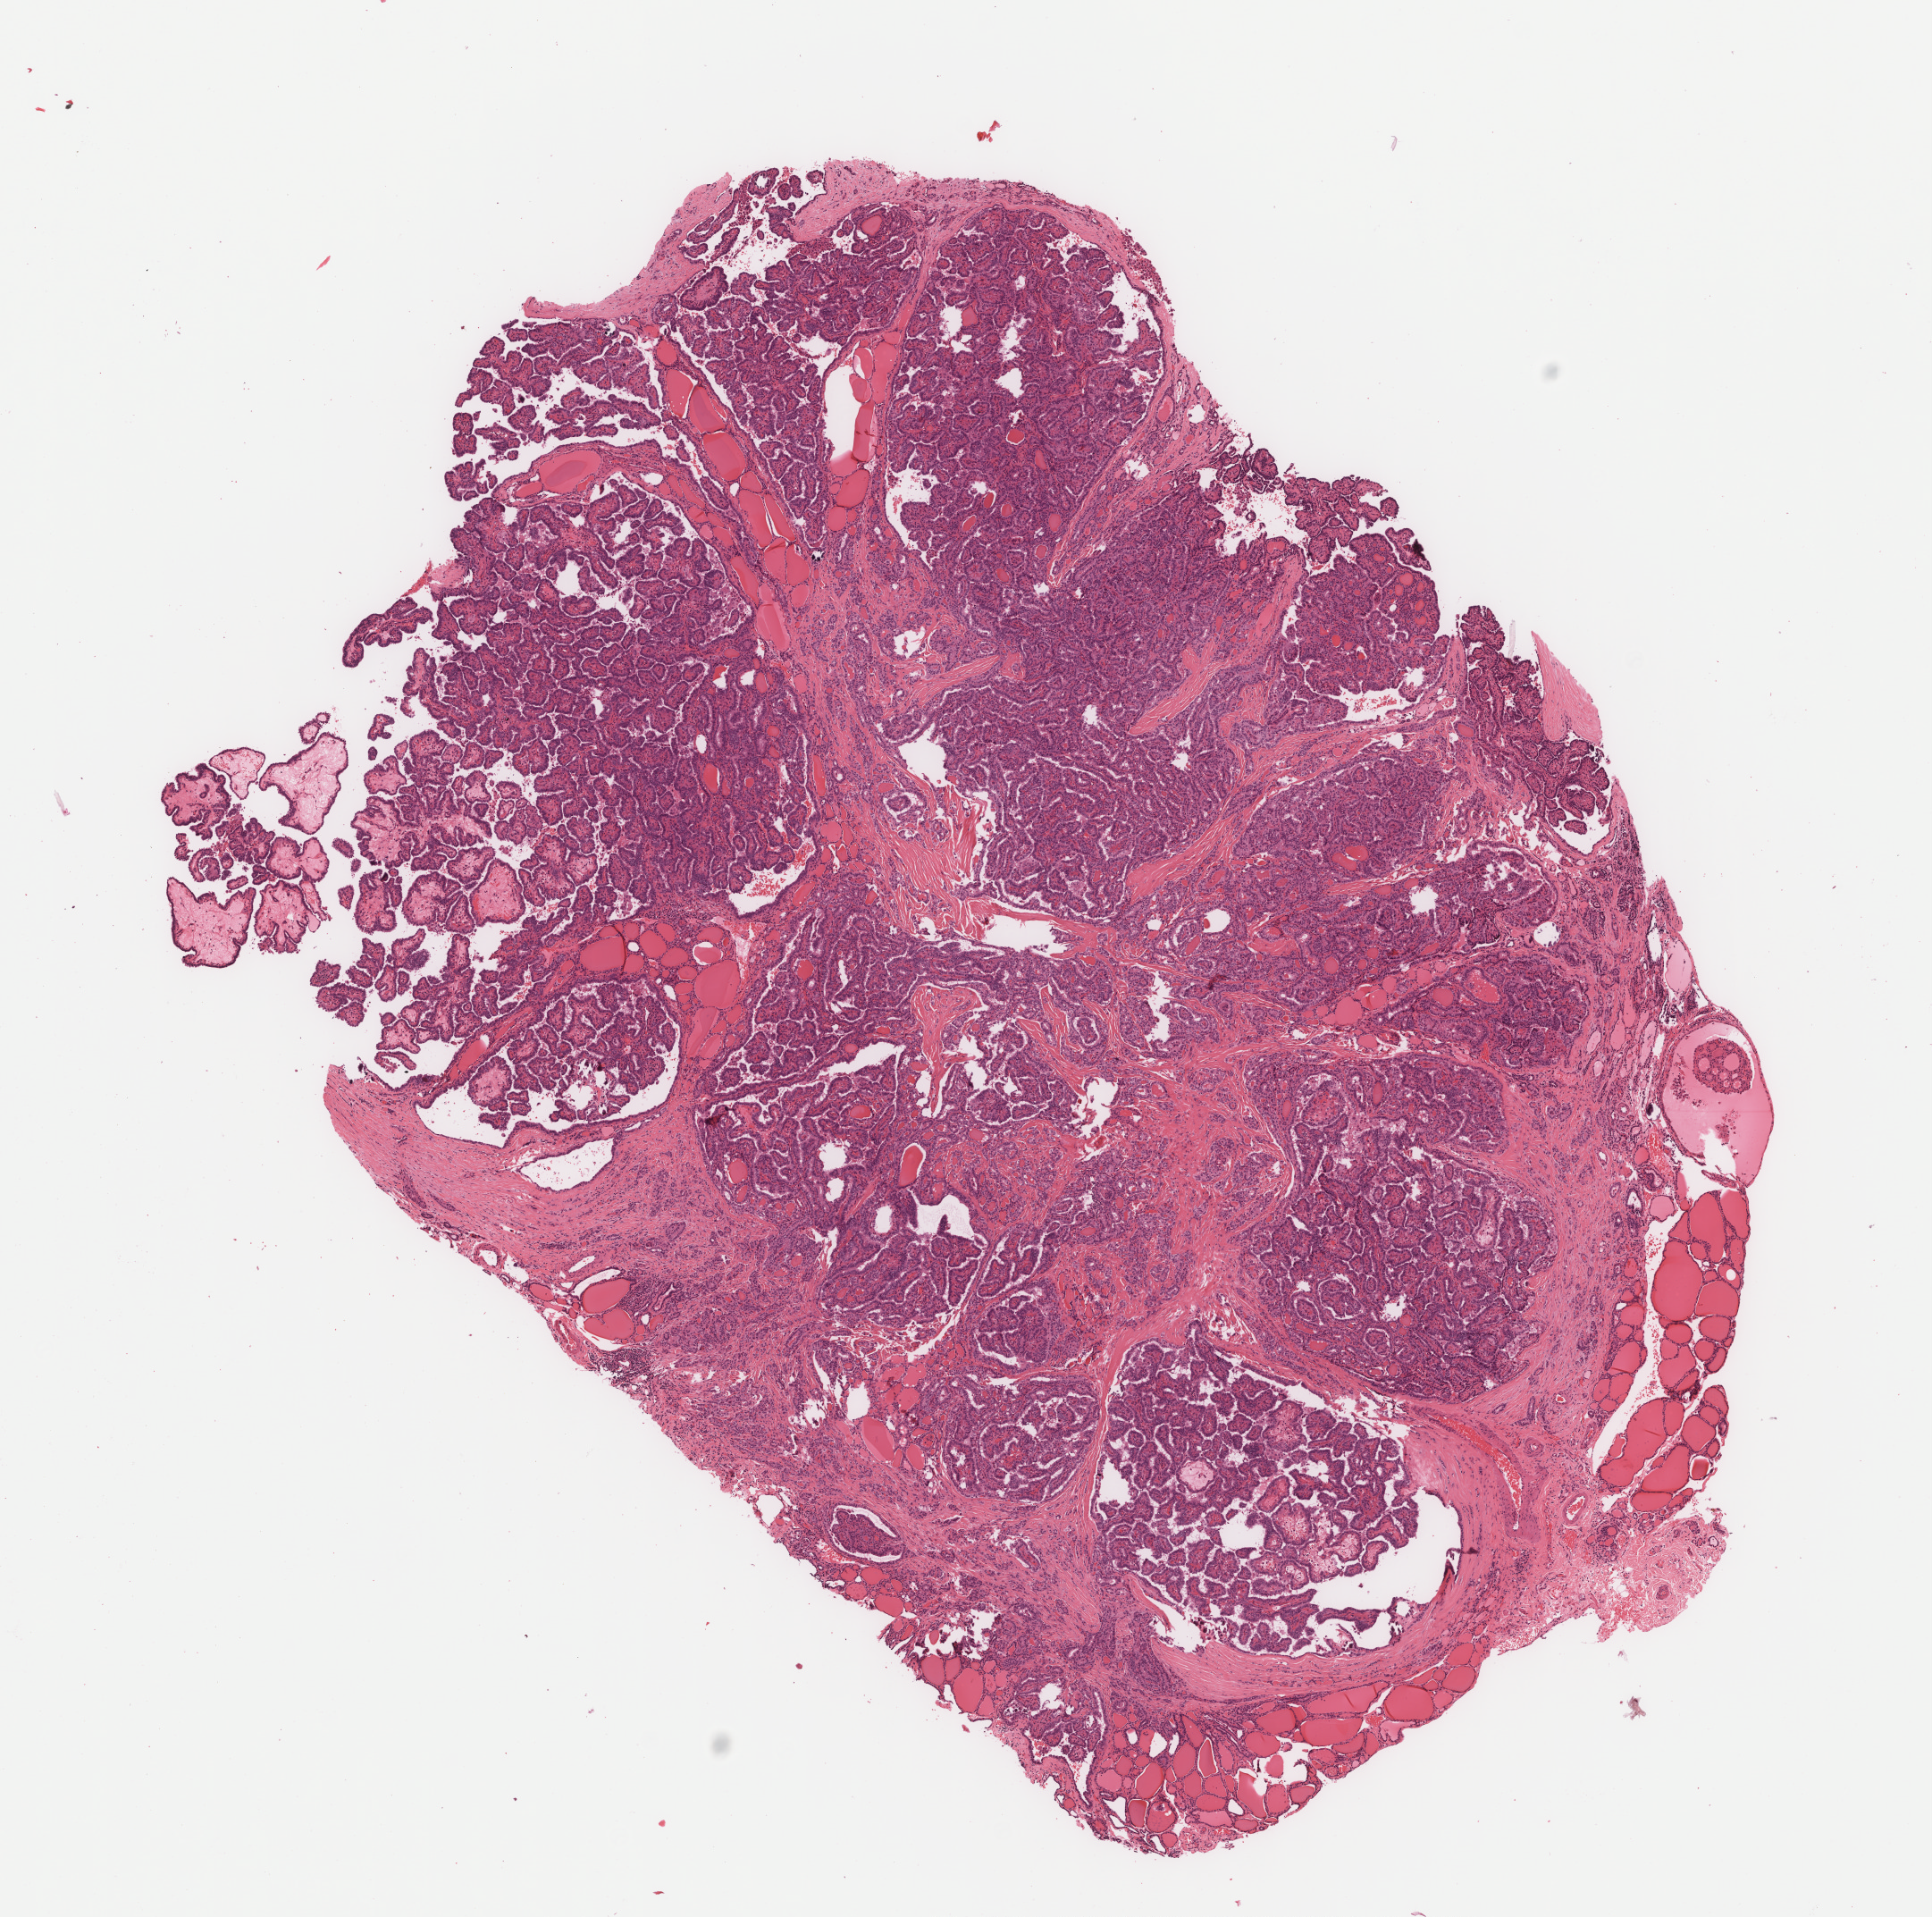
H&E-stained whole-slide image — shown as a low-resolution overview of the whole scanned area (about 8.7 x 8.6 mm, from a 40x scan), formalin-fixed paraffin-embedded (FFPE) diagnostic section, primary tumour sample from the thyroid. Female, age 24 years at initial diagnosis.
* AJCC pathologic stage: I (7th edition)
* TNM: T1a N1b MX
* diagnosis: Papillary adenocarcinoma, NOS (thyroid gland)
* lymph nodes positive (case pathology): 12 of 33 examined